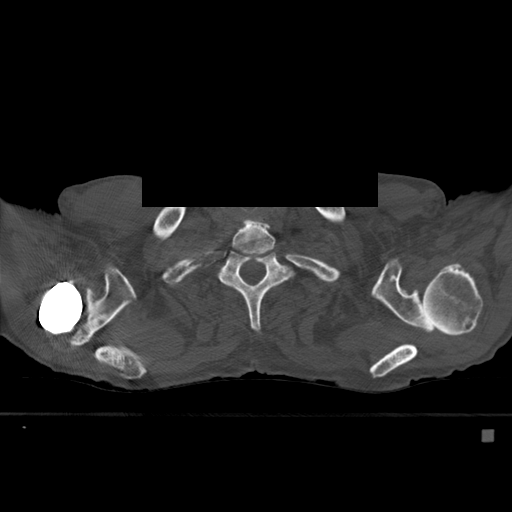
CT including the spine, one axial slice; position 448 of 527 along the scan axis; bone window (W 1800 / L 400 HU); 512 × 512 image matrix. Patient: male, 78 years. Case-level facts recorded for this patient, not image findings: primary cancer: prostate.
Structures marked on this image (semi-automatically segmented with operator editing):
- T1 vertebra: bounding box [x1, y1, x2, y2] px = [232, 227, 275, 253]
- T2 vertebra: [219, 247, 293, 330]